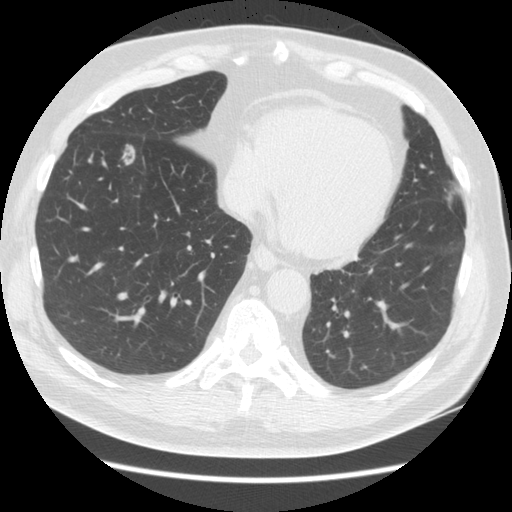
Low-dose screening chest CT, one axial slice; position 52 of 161 along the scan axis; reconstruction kernel STANDARD; lung window (W 1500 / L -600 HU); 2.5 mm slice thickness; 512 × 512 image matrix, field of view 360 × 360 mm.
Structures marked on this image (outlined manually by an expert reader):
- lesion 1 (tumor, lower lobe of right lung): bounding box <122,144,135,165> (left, top, right, bottom; pixels)